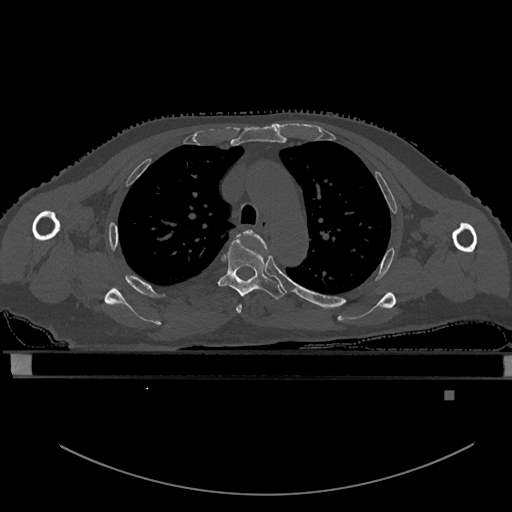
CT including the spine, one axial slice. Position 413 of 969 along the scan axis. Bone window (W 1800 / L 400 HU). 0.5 mm slice thickness. 512 × 512 image matrix. Male patient, age 82 years. Case-level facts recorded for this patient, not image findings: primary cancer: prostate; vertebrae with lytic lesions (as recorded): T11, T9, T8, T2.
Annotated regions visible in this slice (semi-automatically segmented with operator editing):
- T3 vertebra: bounding box (x1, y1, x2, y2) in pixels: (236, 230, 268, 313)
- T4 vertebra: (218, 238, 284, 299)